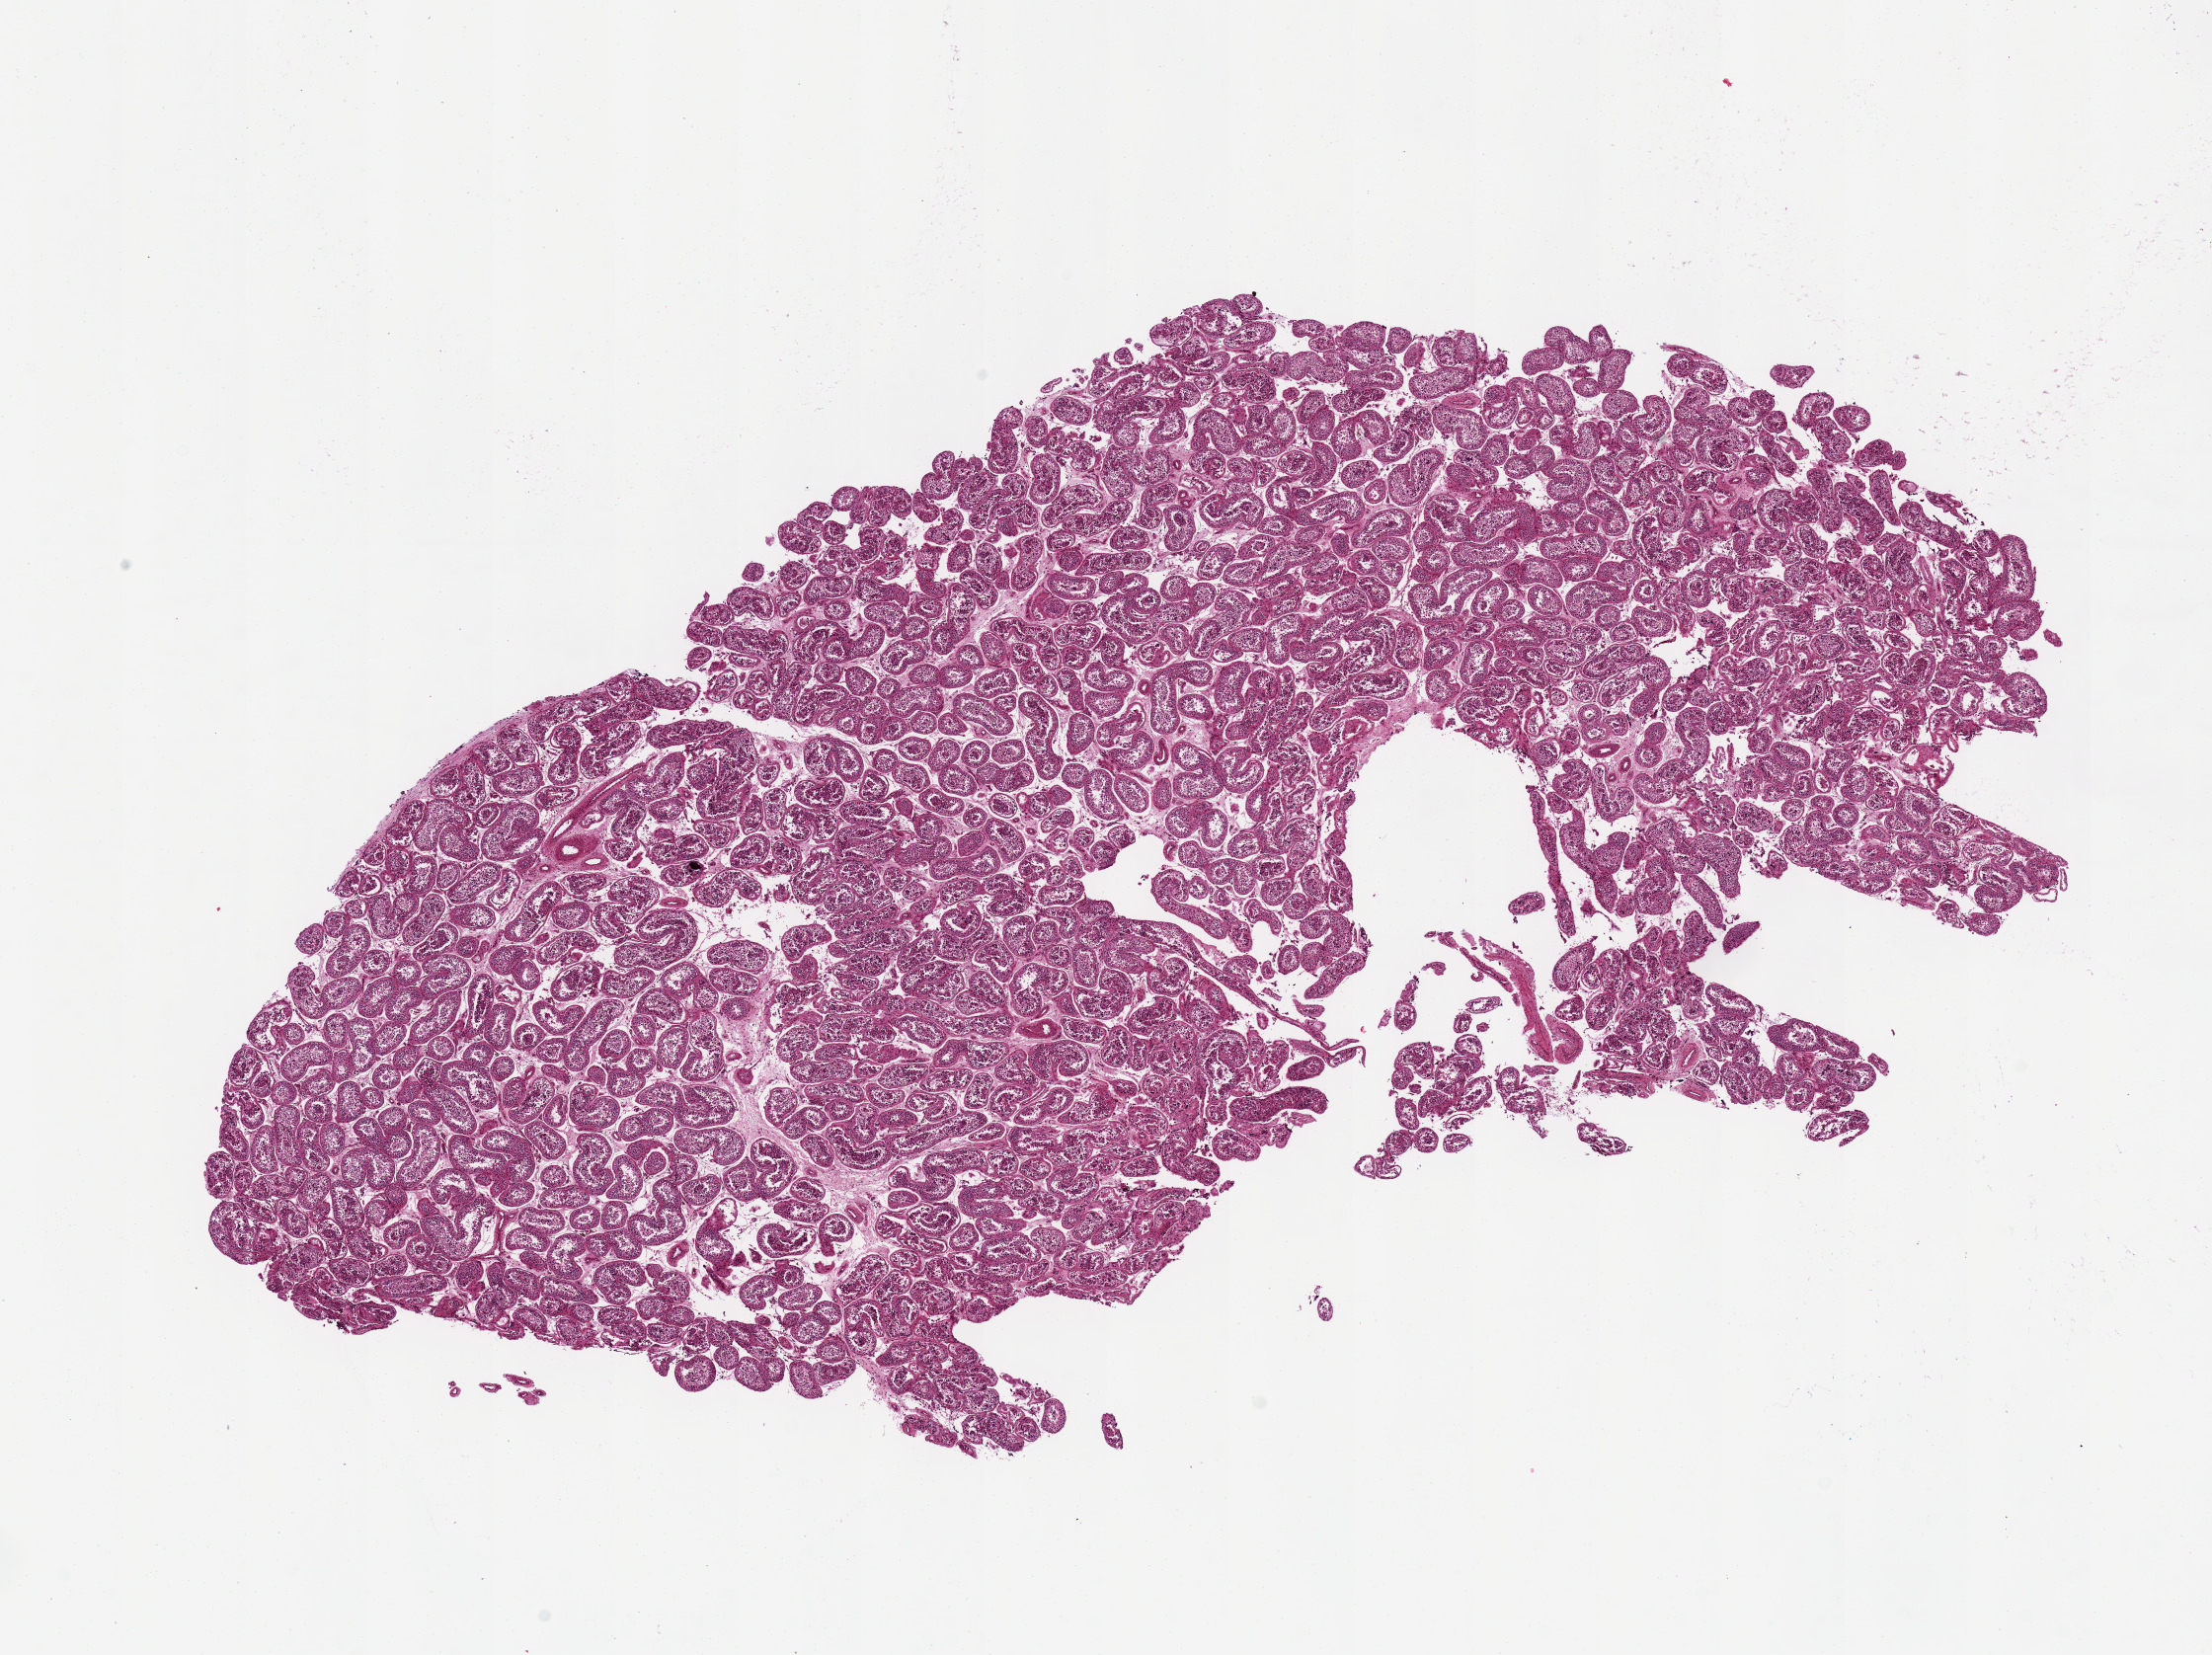
Haematoxylin and eosin whole-slide image, brightfield — low-resolution overview of the scanned area, about 17.7 x 13.3 mm (acquisition: 20x scan). PAXgene-fixed, paraffin-embedded tissue. Target tissue: testis. Donor tissue sample. Donor: male.
Reviewer comment on this tissue sample: good clean specimen; all parenchyma.